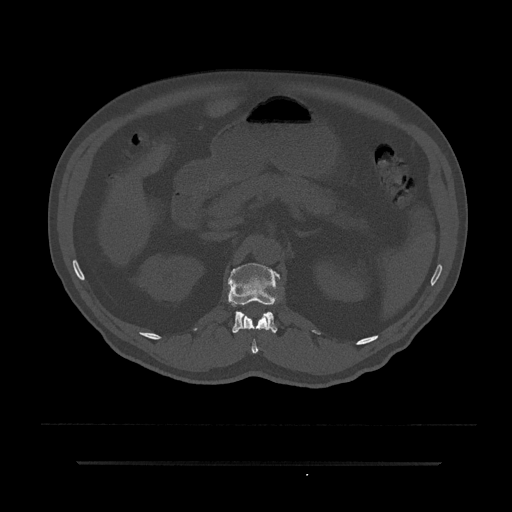
CT including the spine, one axial slice; position 175 of 797 along the scan axis; 120 kVp; bone window (W 1800 / L 400 HU); 512 × 512 image matrix, field of view 464 × 464 mm. Male patient, age 59 years. From the clinical record (not read from this slice): primary cancer: bile ducts; vertebrae with lytic lesions (as recorded): T10.
Annotated regions visible in this slice (semi-automatic segmentation, software-assisted and operator-edited):
- L1 vertebra: bounding box (x1, y1, x2, y2) in pixels: (228, 263, 280, 333)
- T12 vertebra: (240, 315, 268, 354)